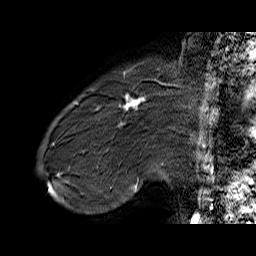
Breast MRI (dynamic contrast-enhanced), one sagittal slice; slice 13 of 60 in the series (ordered by position); dynamic contrast-enhanced series, time point 2 of 6 at this slice position (early post-contrast); 1.5 T; TE 6.4 ms, TR 32.9 ms; 4 mm slice thickness; 256 × 256 image matrix. Female patient. Case-level facts recorded for this patient, not image findings: setting: breast cancer imaged before/during neoadjuvant chemotherapy; receptor status: HER2-positive.
Structures marked on this image (semi-automatically segmented with operator editing):
- analysis volume of interest (the breast-tissue region the enhancement analysis was run in; not a lesion): bounding box (x1, y1, x2, y2) in pixels: (71, 80, 155, 146)
- tumour enhancement mask (voxels above the 100 % enhancement threshold inside the analysis volume of interest): (97, 95, 146, 125)